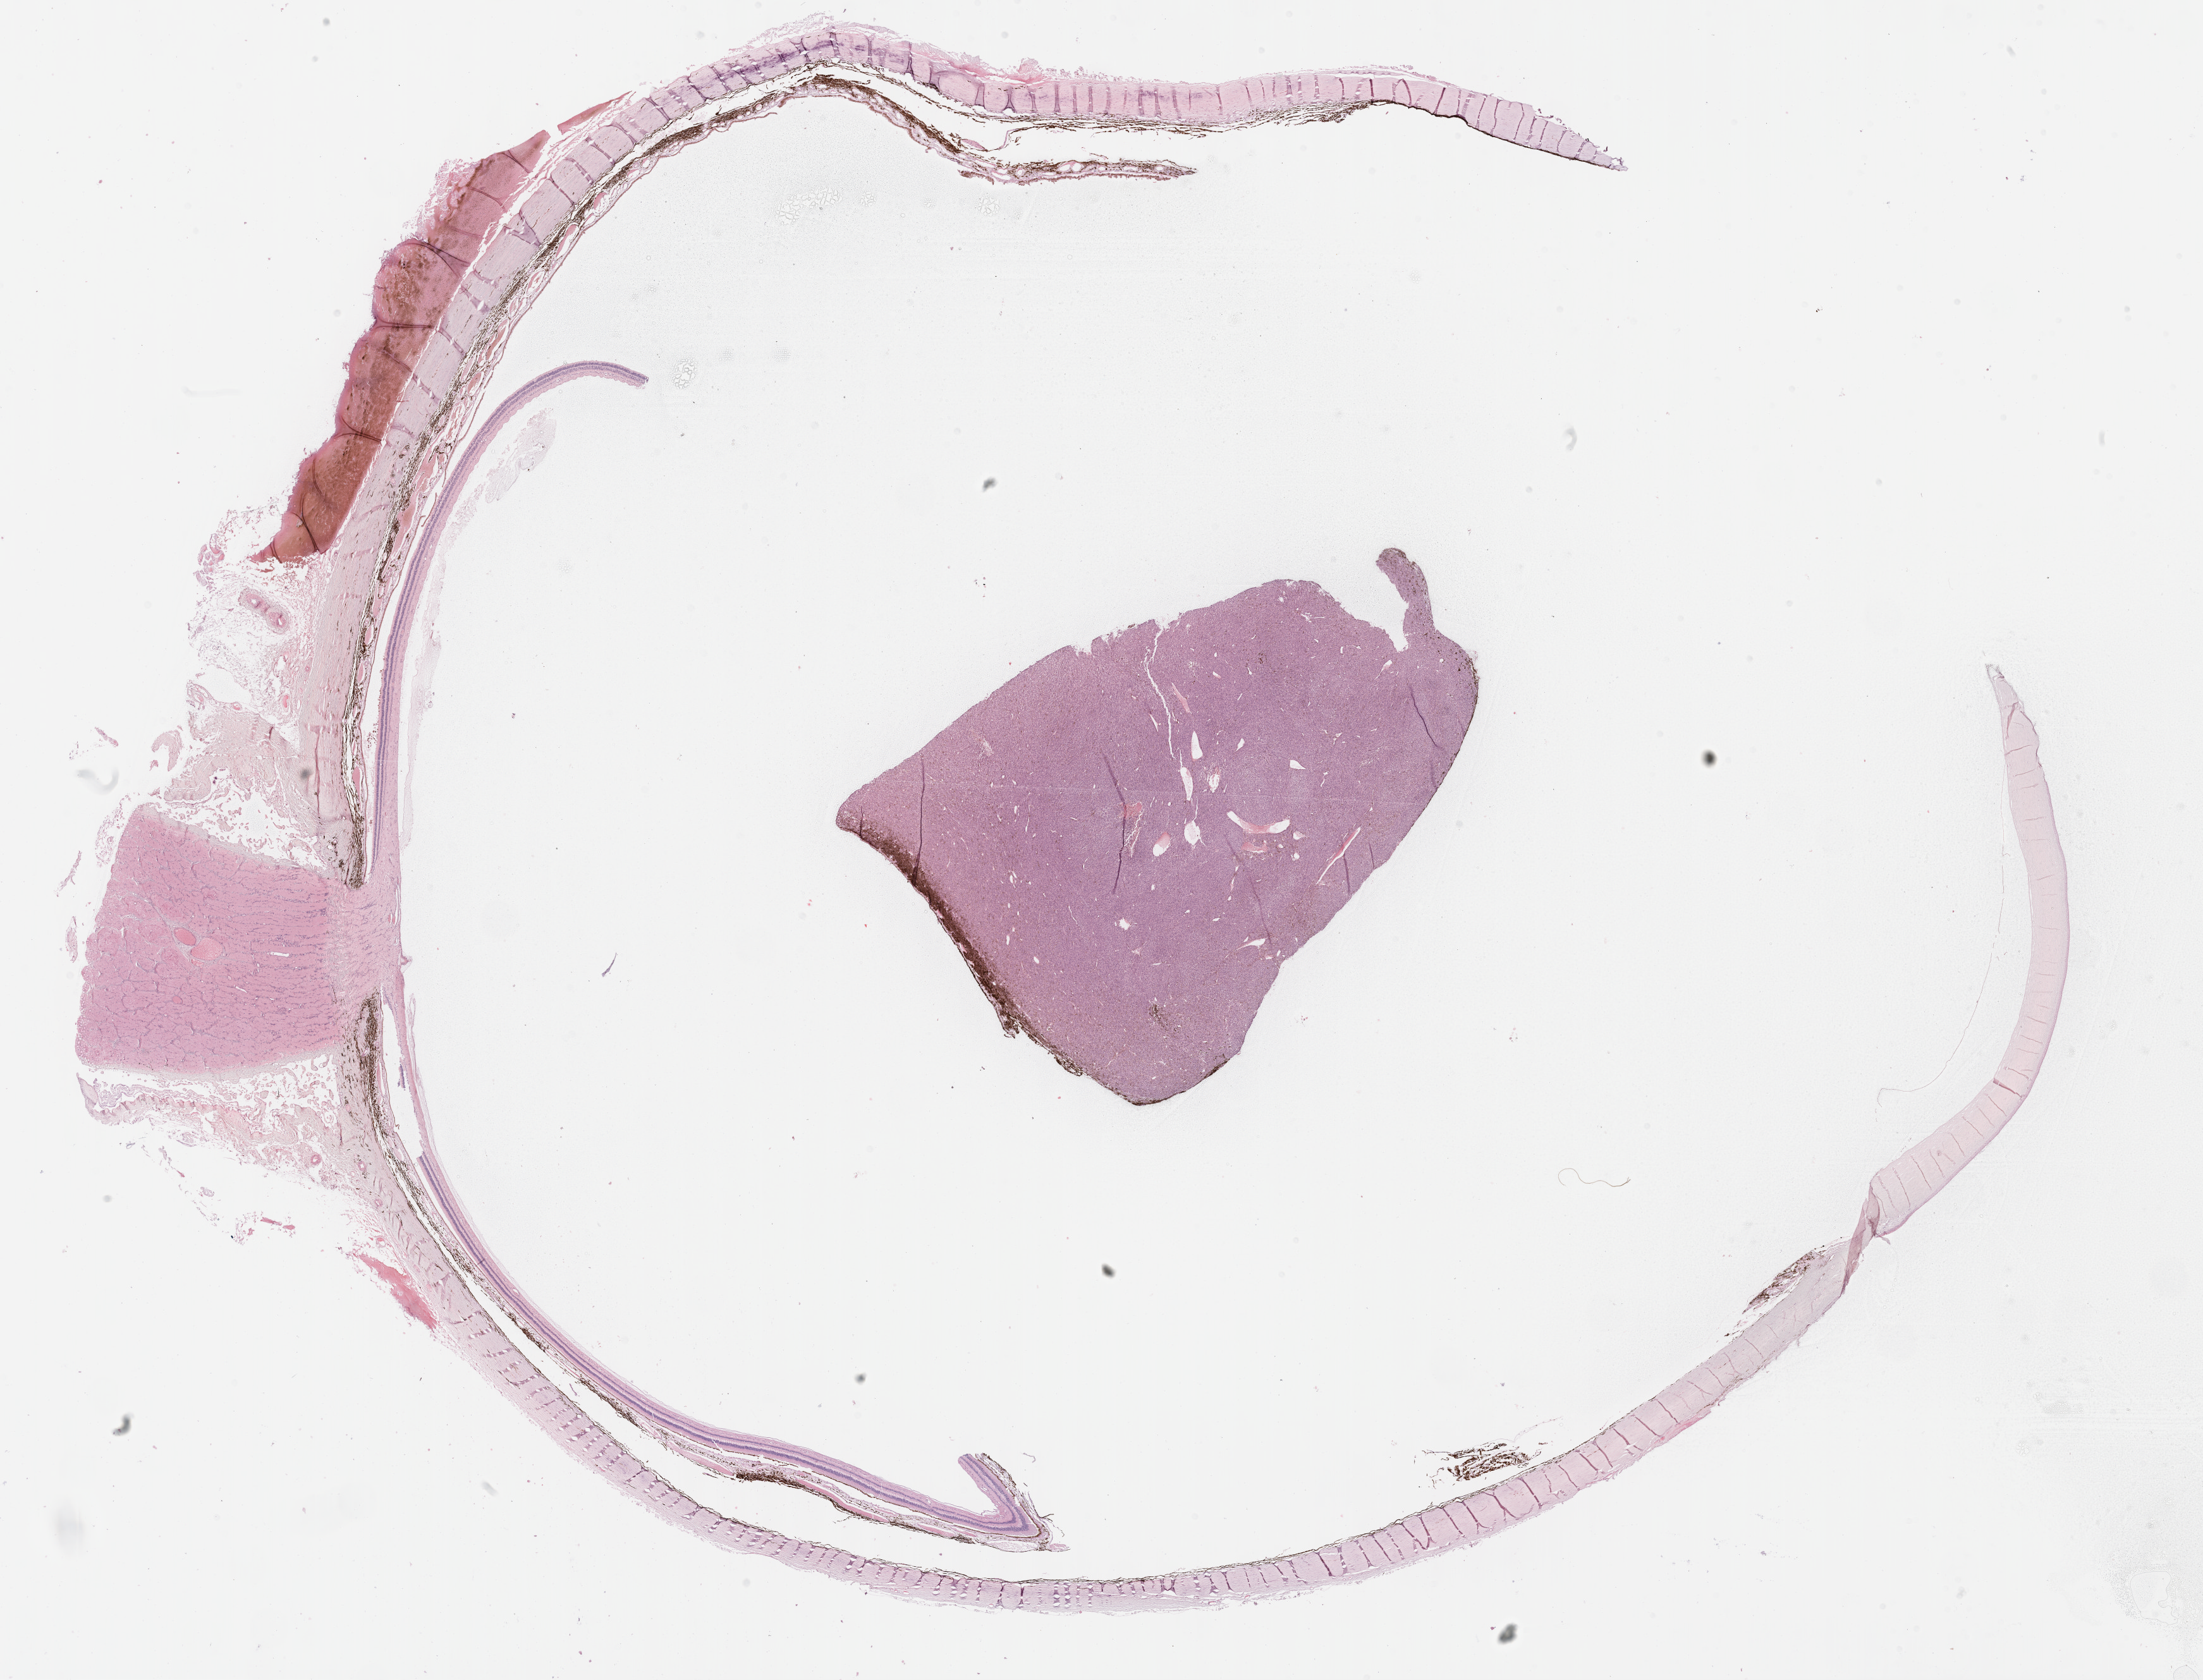
H&E whole-slide image, shown as a low-resolution overview of the whole scanned area (about 28.2 x 21.5 mm); formalin-fixed paraffin-embedded (FFPE) diagnostic section; sample: primary tumour, uvea. Female, age 54 years at initial diagnosis.
Histologic diagnosis: Mixed epithelioid and spindle cell melanoma.